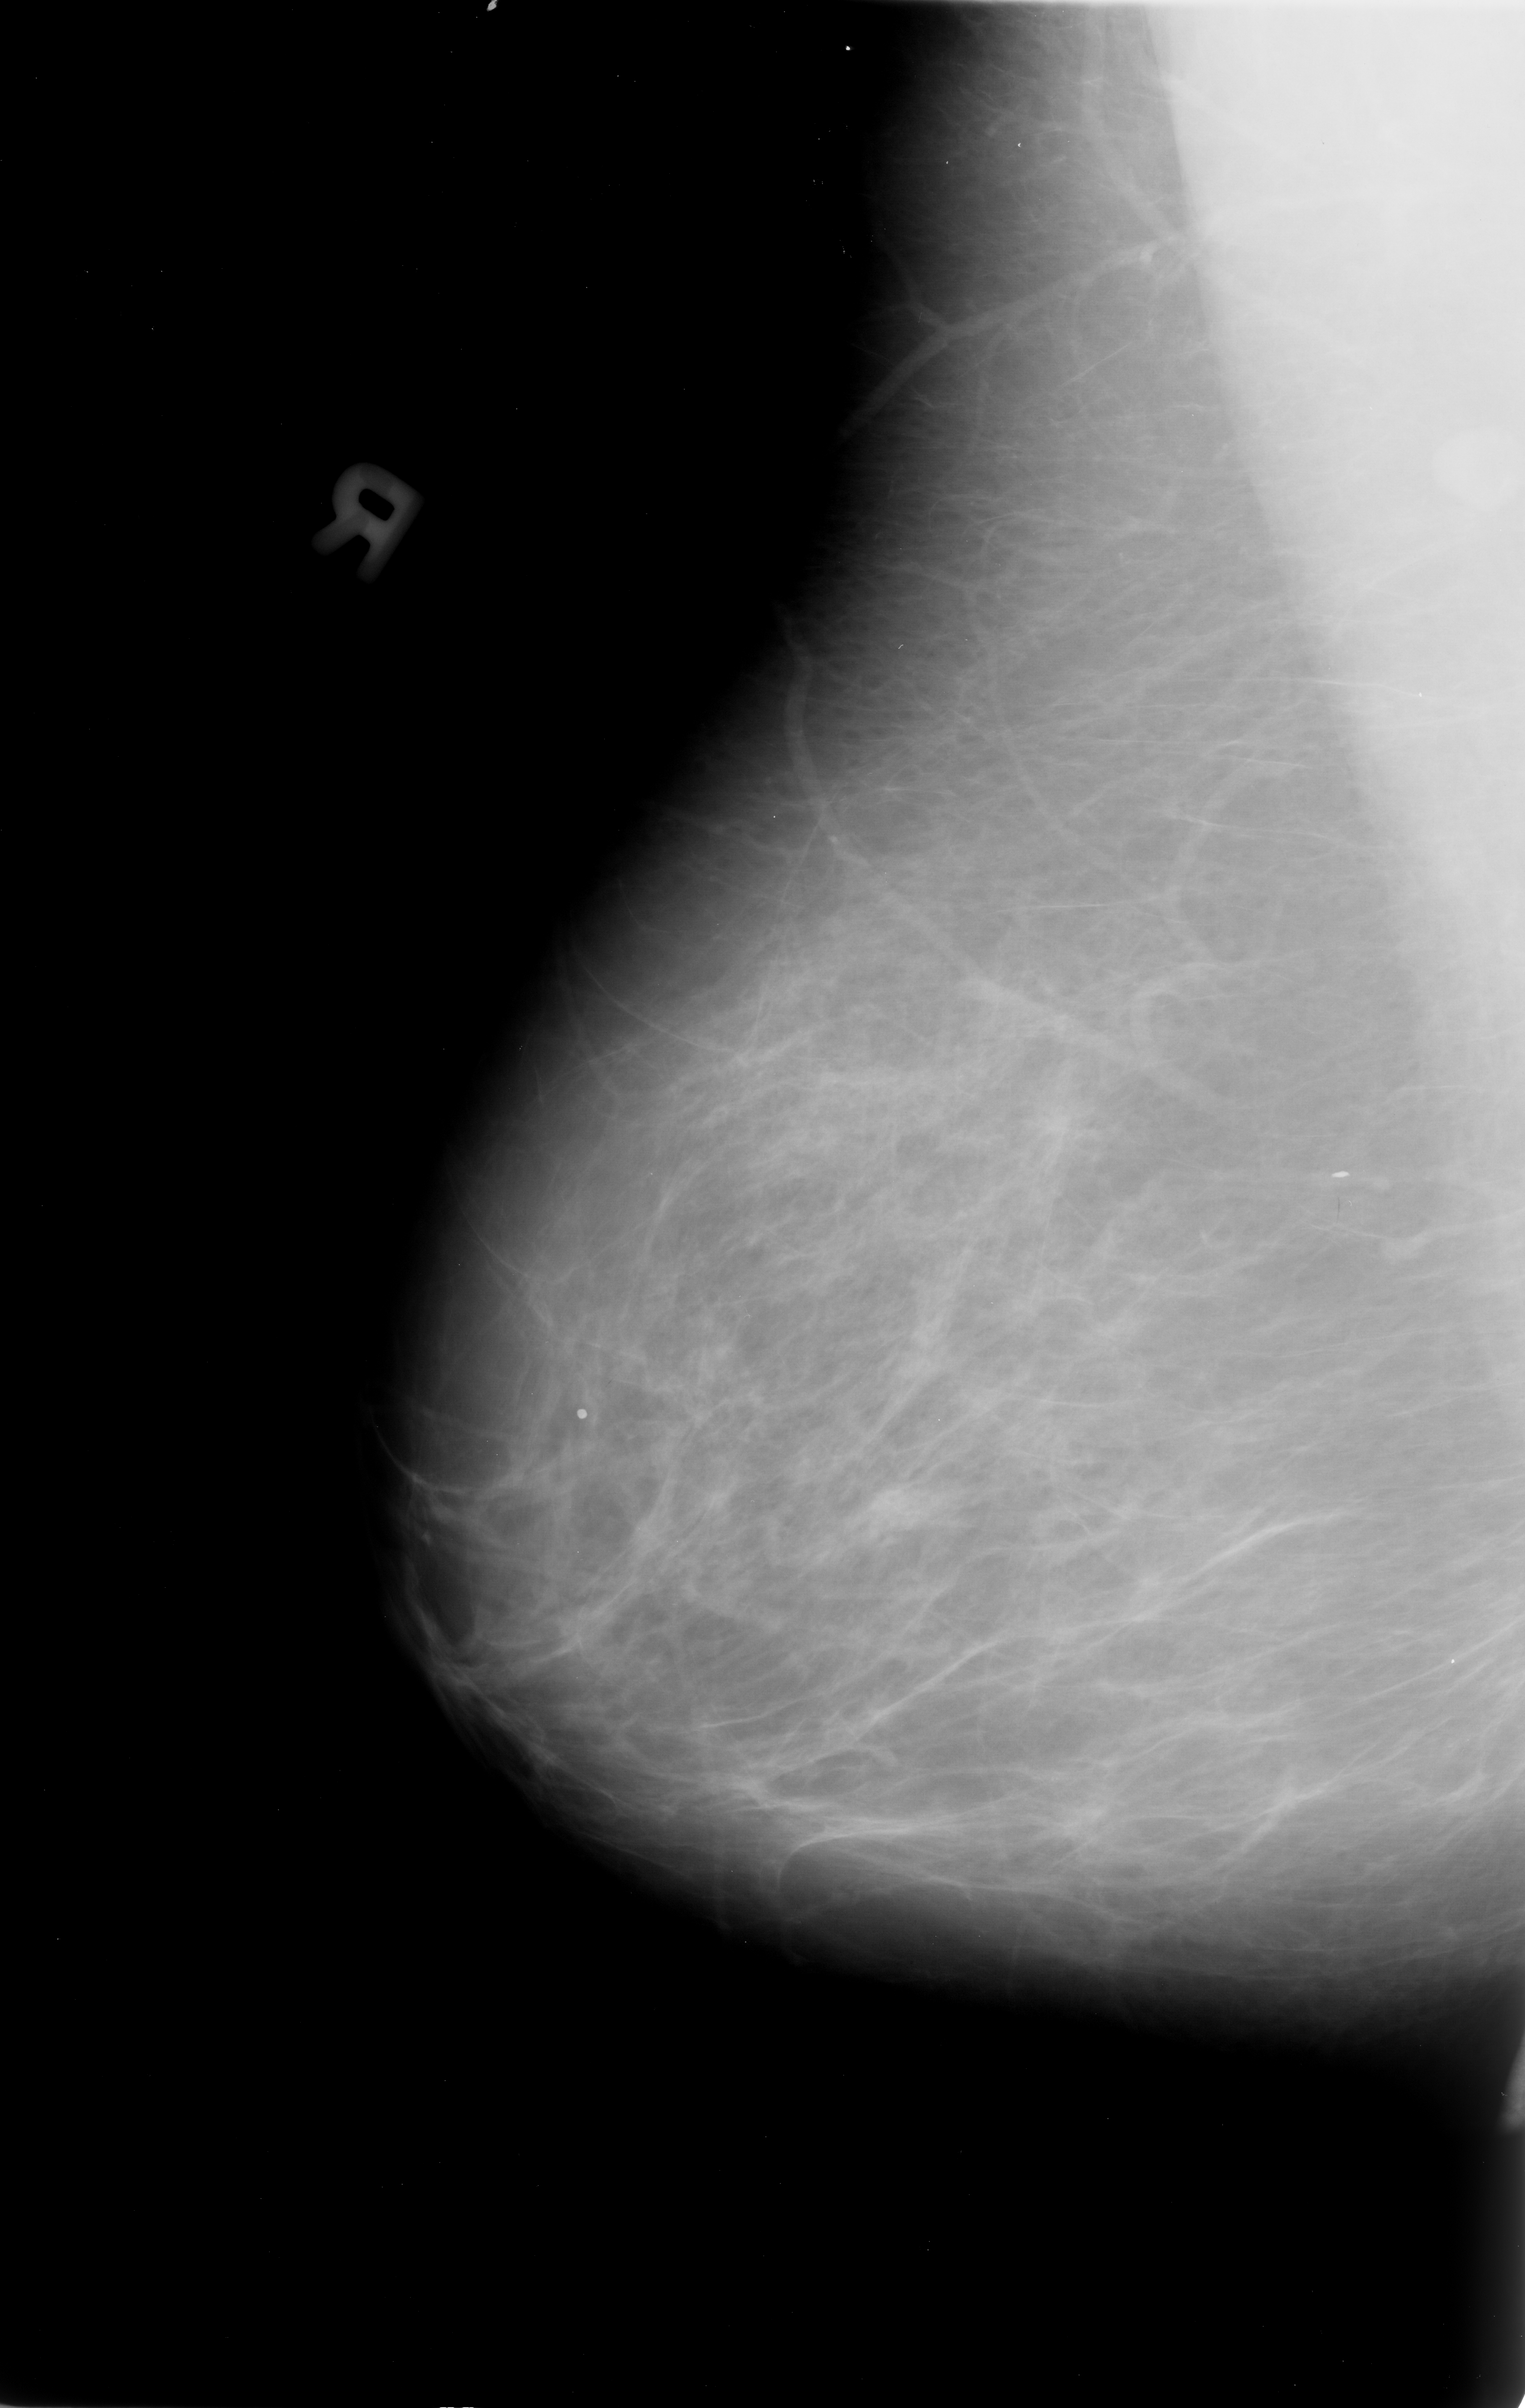
Mammogram (digitized film). Right breast. MLO view. Breast composition: almost entirely fatty (BI-RADS density category 1 of 4). 1525 × 2408 image matrix.
Marked abnormalities (boxes around the expert regions of interest):
- Finding 1 of 2: calcifications, morphology coarse; BI-RADS assessment category 2; benign; no additional work-up was recommended (outcome (as recorded, no biopsy): benign without callback): bounding box (x1, y1, x2, y2) in pixels: (550, 1387, 609, 1448)
- Finding 2 of 2: calcifications, morphology vascular; BI-RADS assessment category 2; subtlety rating 3 on a 1 (subtle) to 5 (obvious) scale; benign; no additional work-up was recommended (outcome (as recorded, no biopsy): benign without callback): (1296, 1138, 1365, 1210)